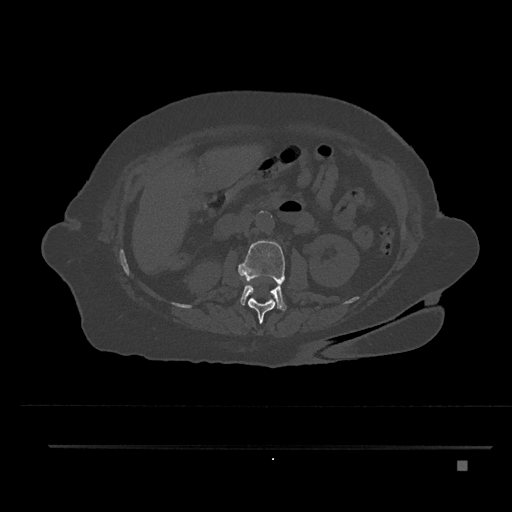
CT including the spine, one axial slice. Position 198 of 797 along the scan axis. Reconstruction kernel Br40s/3. 120 kVp. Bone window (W 1800 / L 400 HU). 0.5 mm slice thickness. 512 × 512 image matrix, field of view 437 × 437 mm. Patient: female, 76 years. From the clinical record (not read from this slice): primary cancer: lung; vertebrae with lytic lesions (as recorded): T11, L3.
Structures marked on this image (semi-automatically segmented with operator editing):
- L1 vertebra: bounding box <248,298,278,324> (left, top, right, bottom; pixels)
- L2 vertebra: <238,240,286,311>